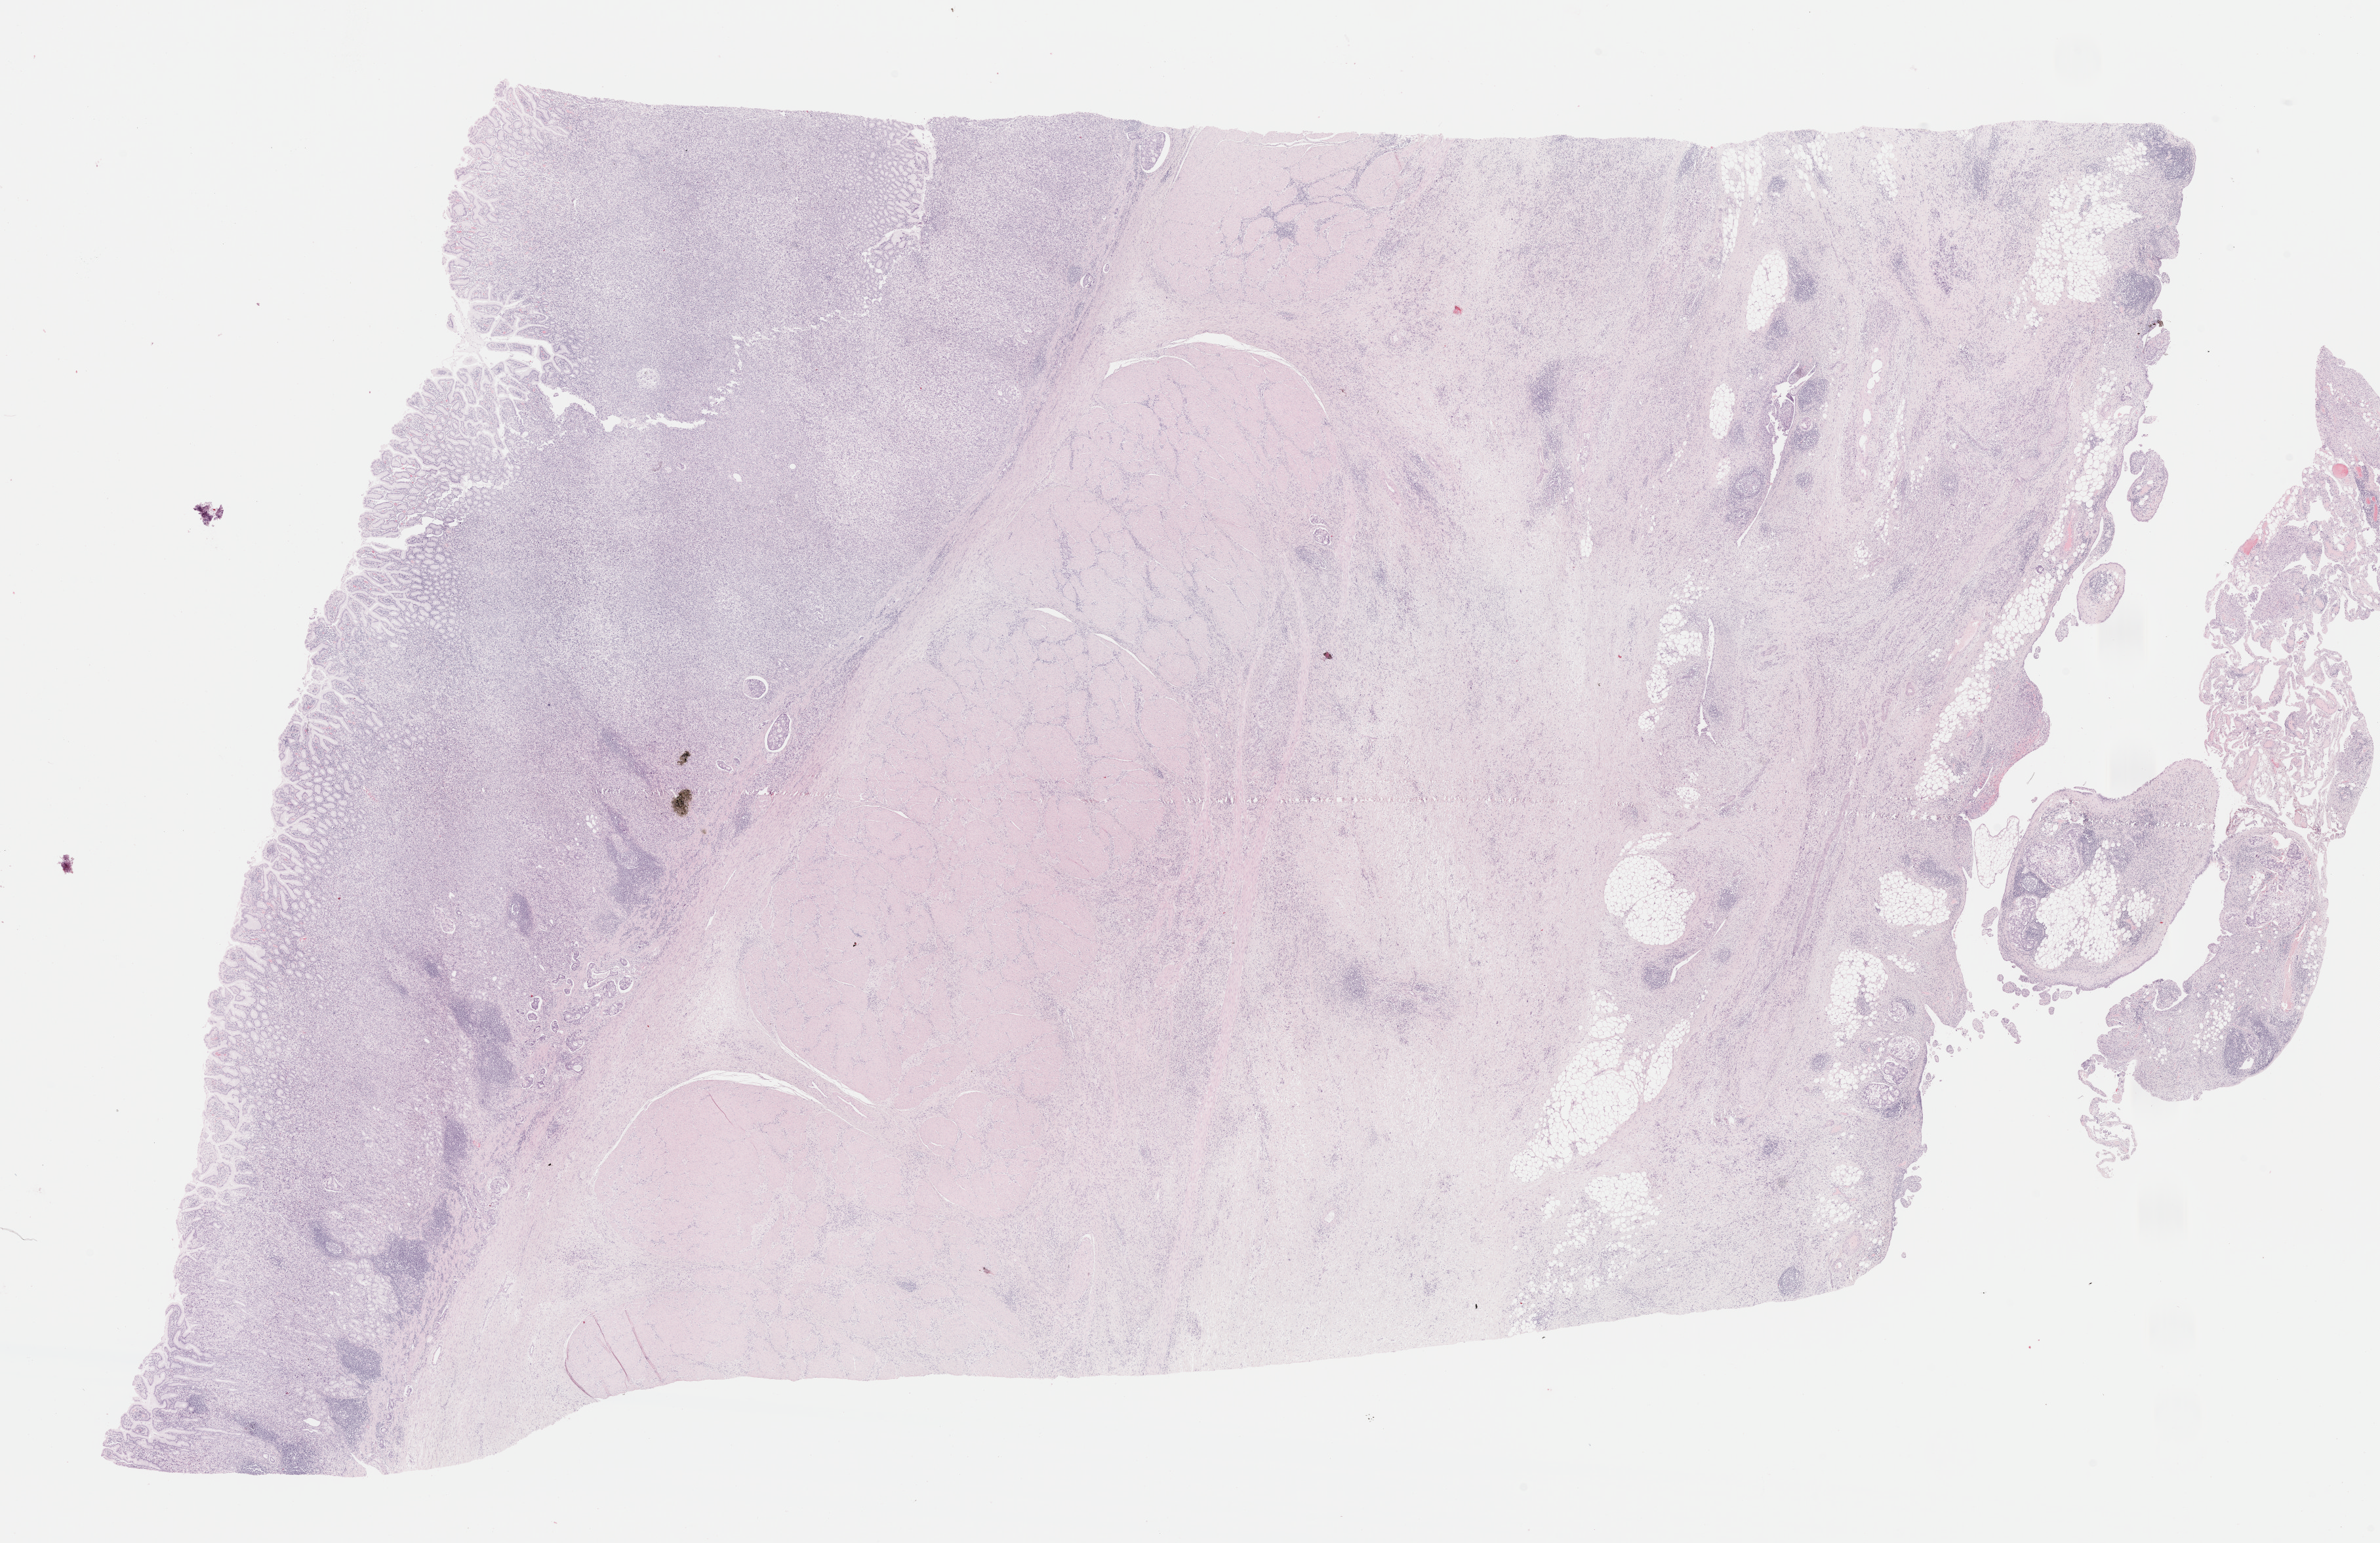
H&E whole-slide image, whole scanned area (about 28.6 x 18.6 mm, from a 40x scan) shown as a low-resolution overview, formalin-fixed paraffin-embedded (FFPE) diagnostic section, sample: primary tumour, stomach. Patient: female, age at initial diagnosis 54 years.
Diagnosis: Tubular adenocarcinoma (gastric antrum).